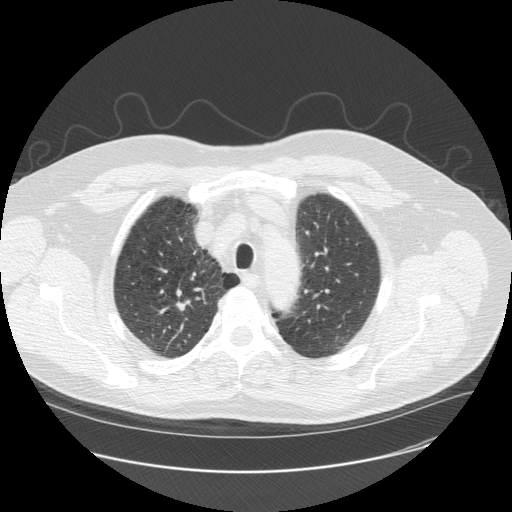
Chest CT (low-dose screening protocol), one axial image. Second annual screen. Lung window (W 1500 / L -600 HU). 2.5 mm slice thickness. Slice 35 of 179 in the series. 512 × 512 image matrix, field of view 400 × 400 mm. Male participant, aged 61 years at enrolment. Former smoker at enrolment.
• Expert-annotated lung lesion, bounding box <160,288,202,328> (left, top, right, bottom; pixels).
• No non-calcified nodule or mass ≥4 mm was recorded by the screening reader at this exam.
• Participant outcome: lung cancer diagnosed 467 days after this screen — squamous cell carcinoma, NOS, right upper lobe, moderately differentiated (G2), stage IA (AJCC 6th edition), 10 mm at pathology.